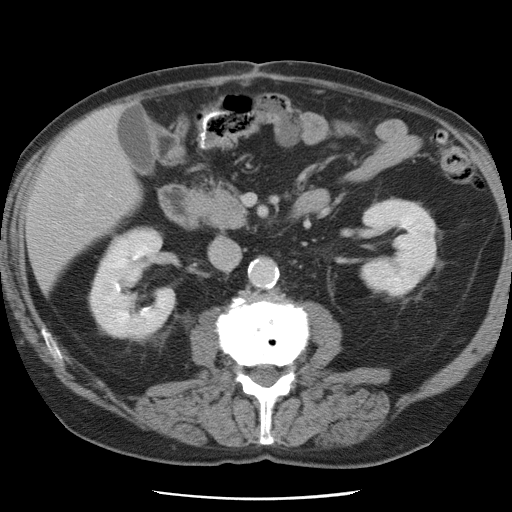
Contrast-enhanced abdominal CT, one axial slice; position 27 of 78 along the scan axis; 120 kVp; intravenous contrast given; soft-tissue window (W 400 / L 40 HU); 512 × 512 image matrix, field of view 337 × 337 mm. Male patient, age 75 years. From the clinical record (not read from this slice): diagnosis: colorectal cancer liver metastases, imaged before liver resection; multiple liver metastases: yes; largest metastasis: 2.4 cm; chemotherapy before resection: yes.
Structures marked on this image (expert manual segmentation):
- liver: box from (x=28, y=107) to (x=140, y=288) px
- planned liver remnant (the part of the liver to remain after resection): (x=28, y=117)–(x=141, y=289)